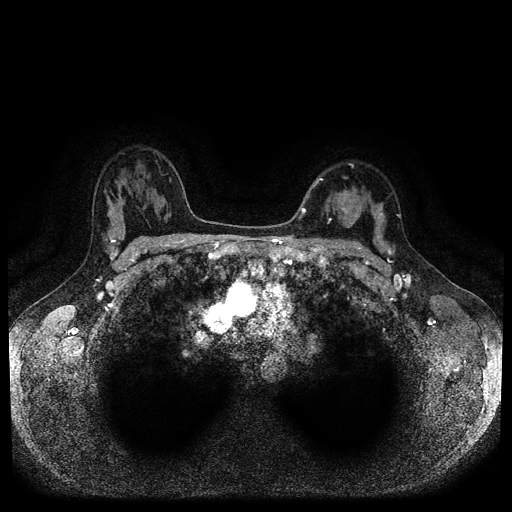
Breast MRI (dynamic contrast-enhanced, multi-phase), one axial slice; position 72 of 116 along the scan axis; dynamic contrast-enhanced series, time point 2 of 5 at this slice position (early post-contrast); 1.5 T; TE 2.6 ms, TR 5.3 ms; 512 × 512 image matrix. Female patient, age 33 years.
Annotated regions visible in this slice (semi-automatically segmented with operator editing):
- breast lesion (labelled 'tumour' in the annotation; benign lesions carry a separate 'benign' label): bounding box (x1, y1, x2, y2) in pixels: (339, 207, 349, 214)